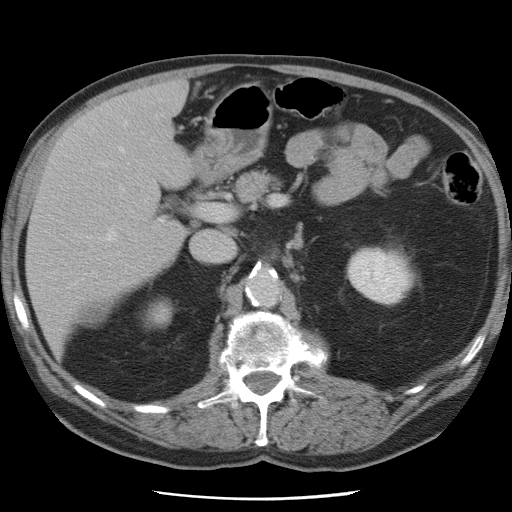
Contrast-enhanced abdominal CT, one axial slice. Position 41 of 78 along the scan axis. Intravenous contrast given. Soft-tissue window (W 400 / L 40 HU). 5 mm slice thickness. 512 × 512 image matrix. Male patient, age 75 years. Case-level facts recorded for this patient, not image findings: diagnosis: colorectal cancer liver metastases, imaged before liver resection; multiple liver metastases: yes; largest metastasis: 2.4 cm; disease in both lobes: yes.
Annotated regions visible in this slice (expert manual segmentation):
- hepatic veins: bounding box [x1, y1, x2, y2] px = [98, 122, 127, 241]
- liver: [28, 83, 191, 346]
- planned liver remnant (the part of the liver to remain after resection): [28, 120, 184, 345]
- portal vein (with intrahepatic branches): [119, 187, 163, 223]